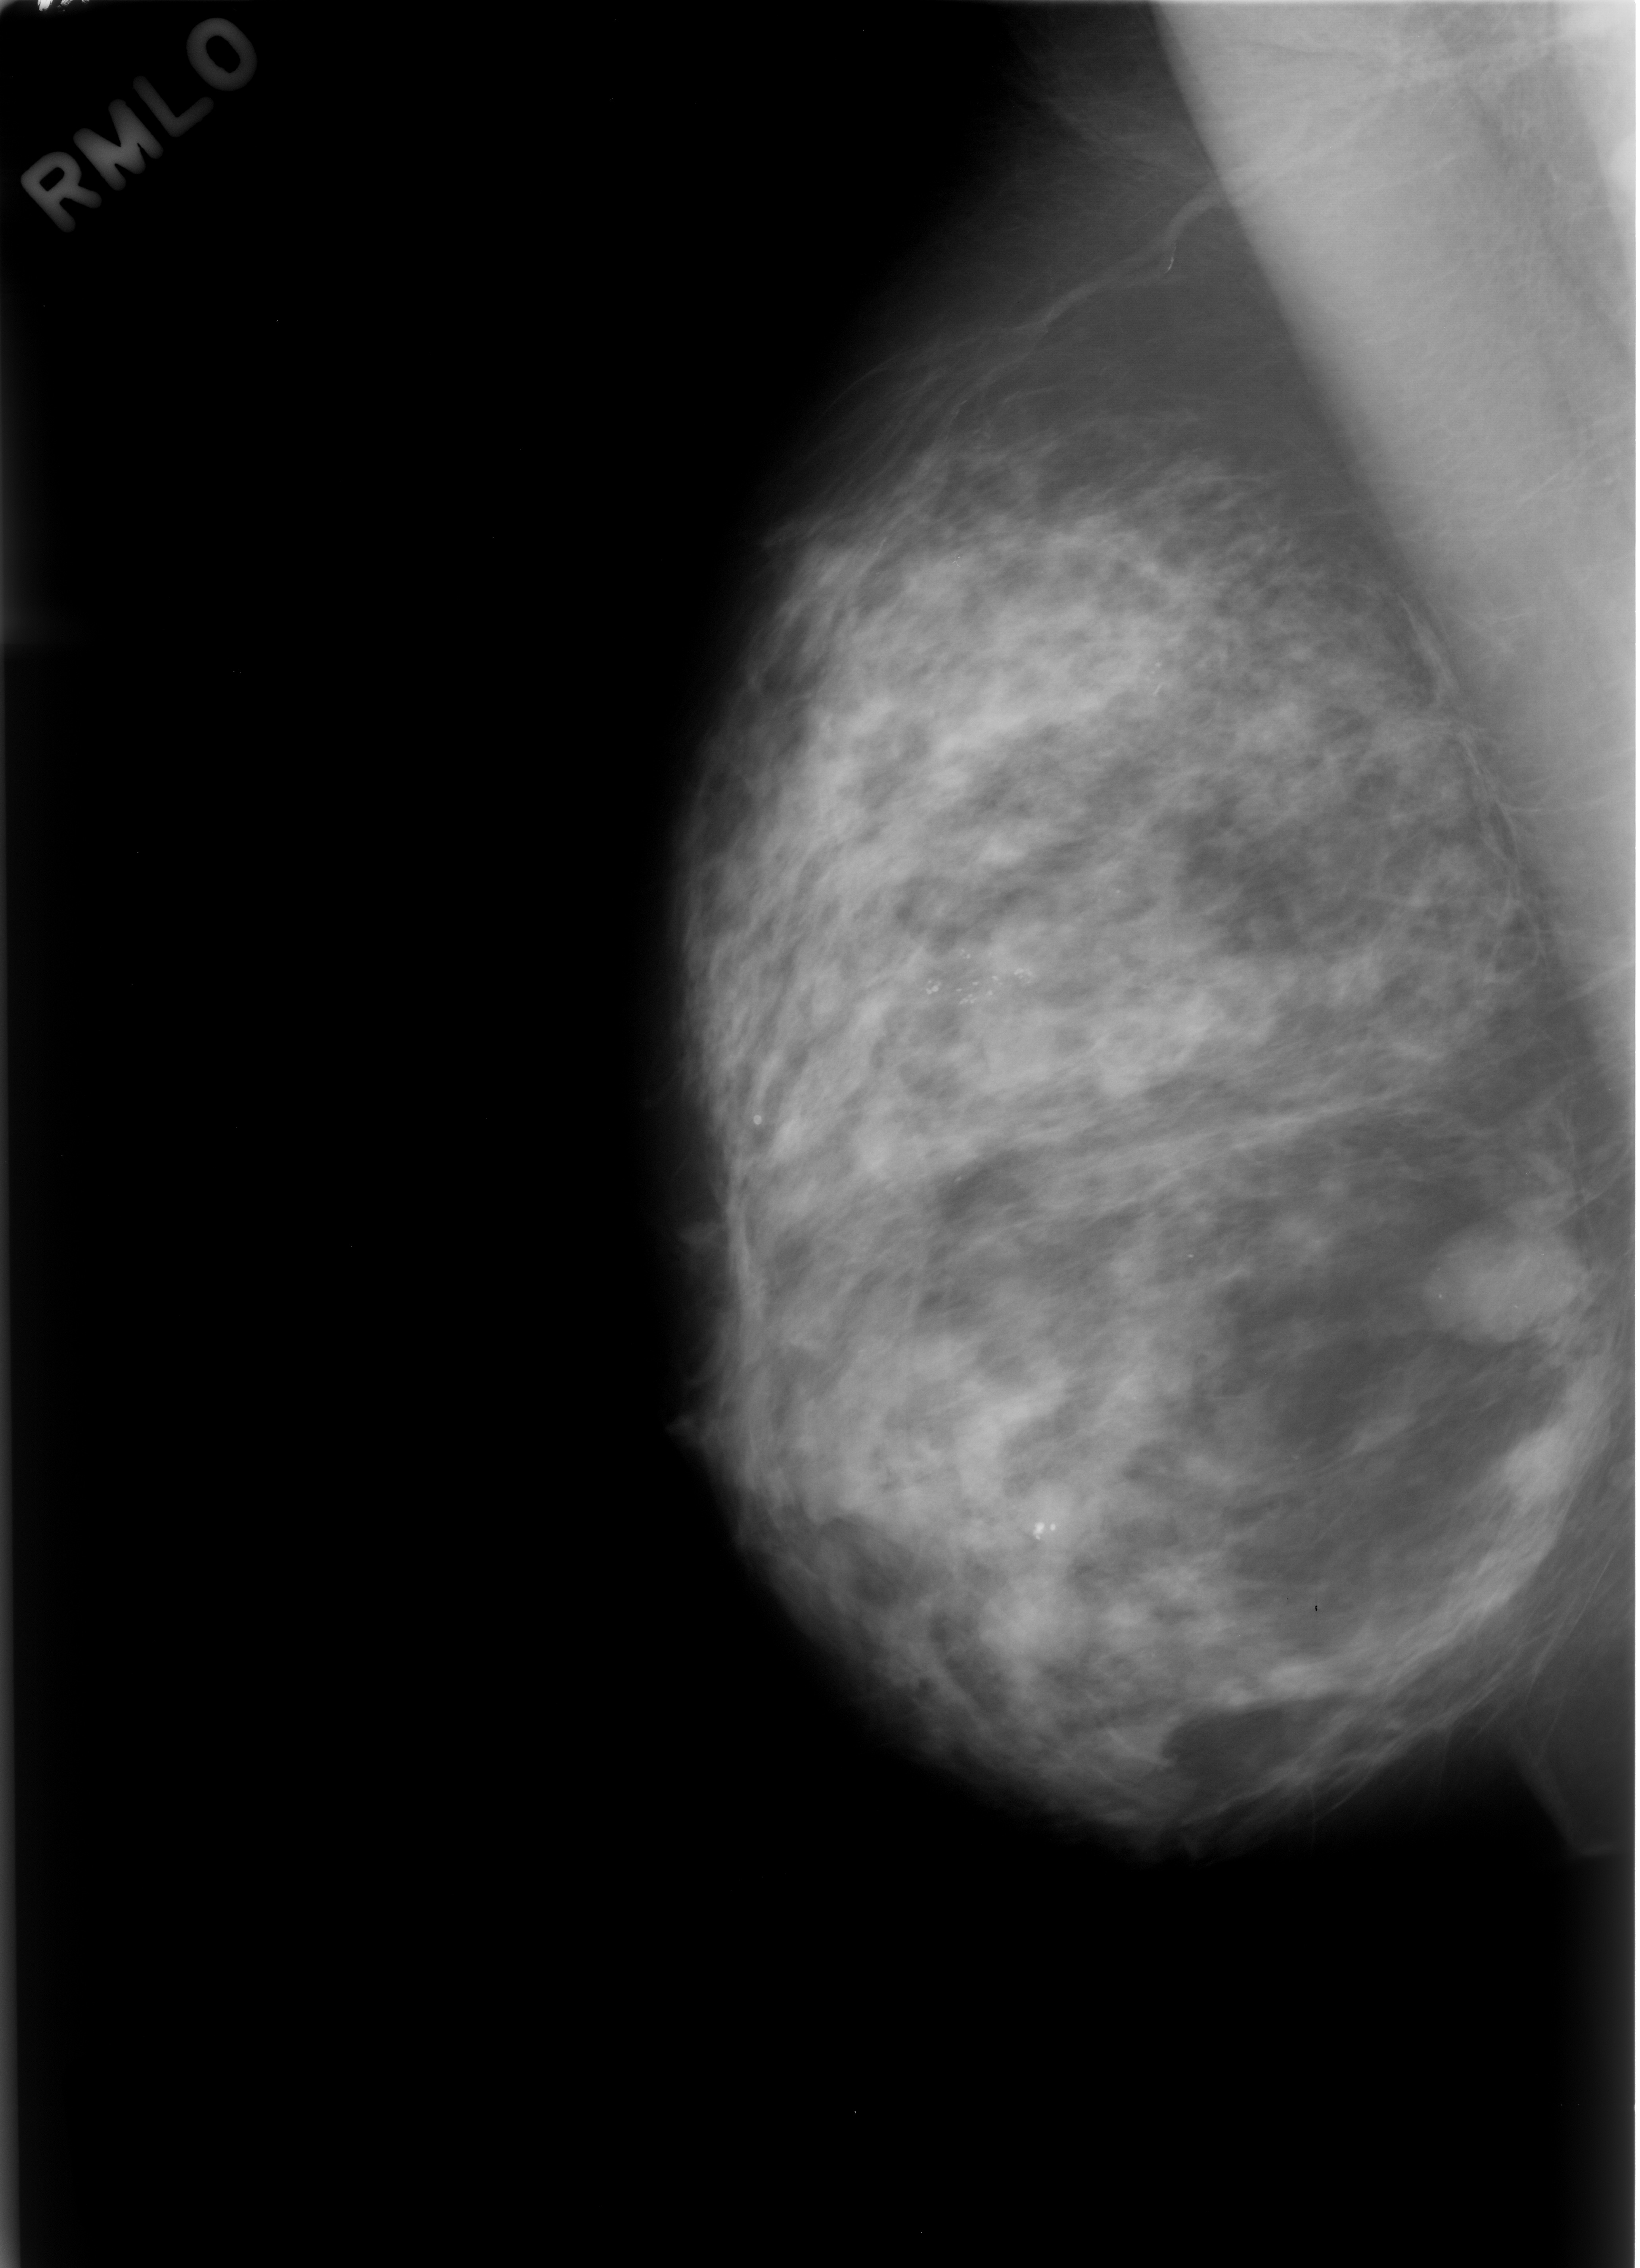
Digitized screen-film mammogram. Right breast. MLO view. Breast composition: heterogeneously dense (BI-RADS density category 3 of 4). 1640 × 2268 image matrix.
Marked abnormalities (boxes around the expert regions of interest):
- Finding 1 of 2: calcifications, morphology pleomorphic, distribution clustered; BI-RADS assessment category 4; subtlety rating 5 on a 1 (subtle) to 5 (obvious) scale; pathology result (as recorded, not read from the image): benign: bounding box (x1, y1, x2, y2) in pixels: (872, 900, 1054, 1073)
- Finding 2 of 2: calcifications, morphology pleomorphic, distribution clustered; BI-RADS assessment category 4; pathology (as recorded): benign: (967, 1459, 1124, 1673)